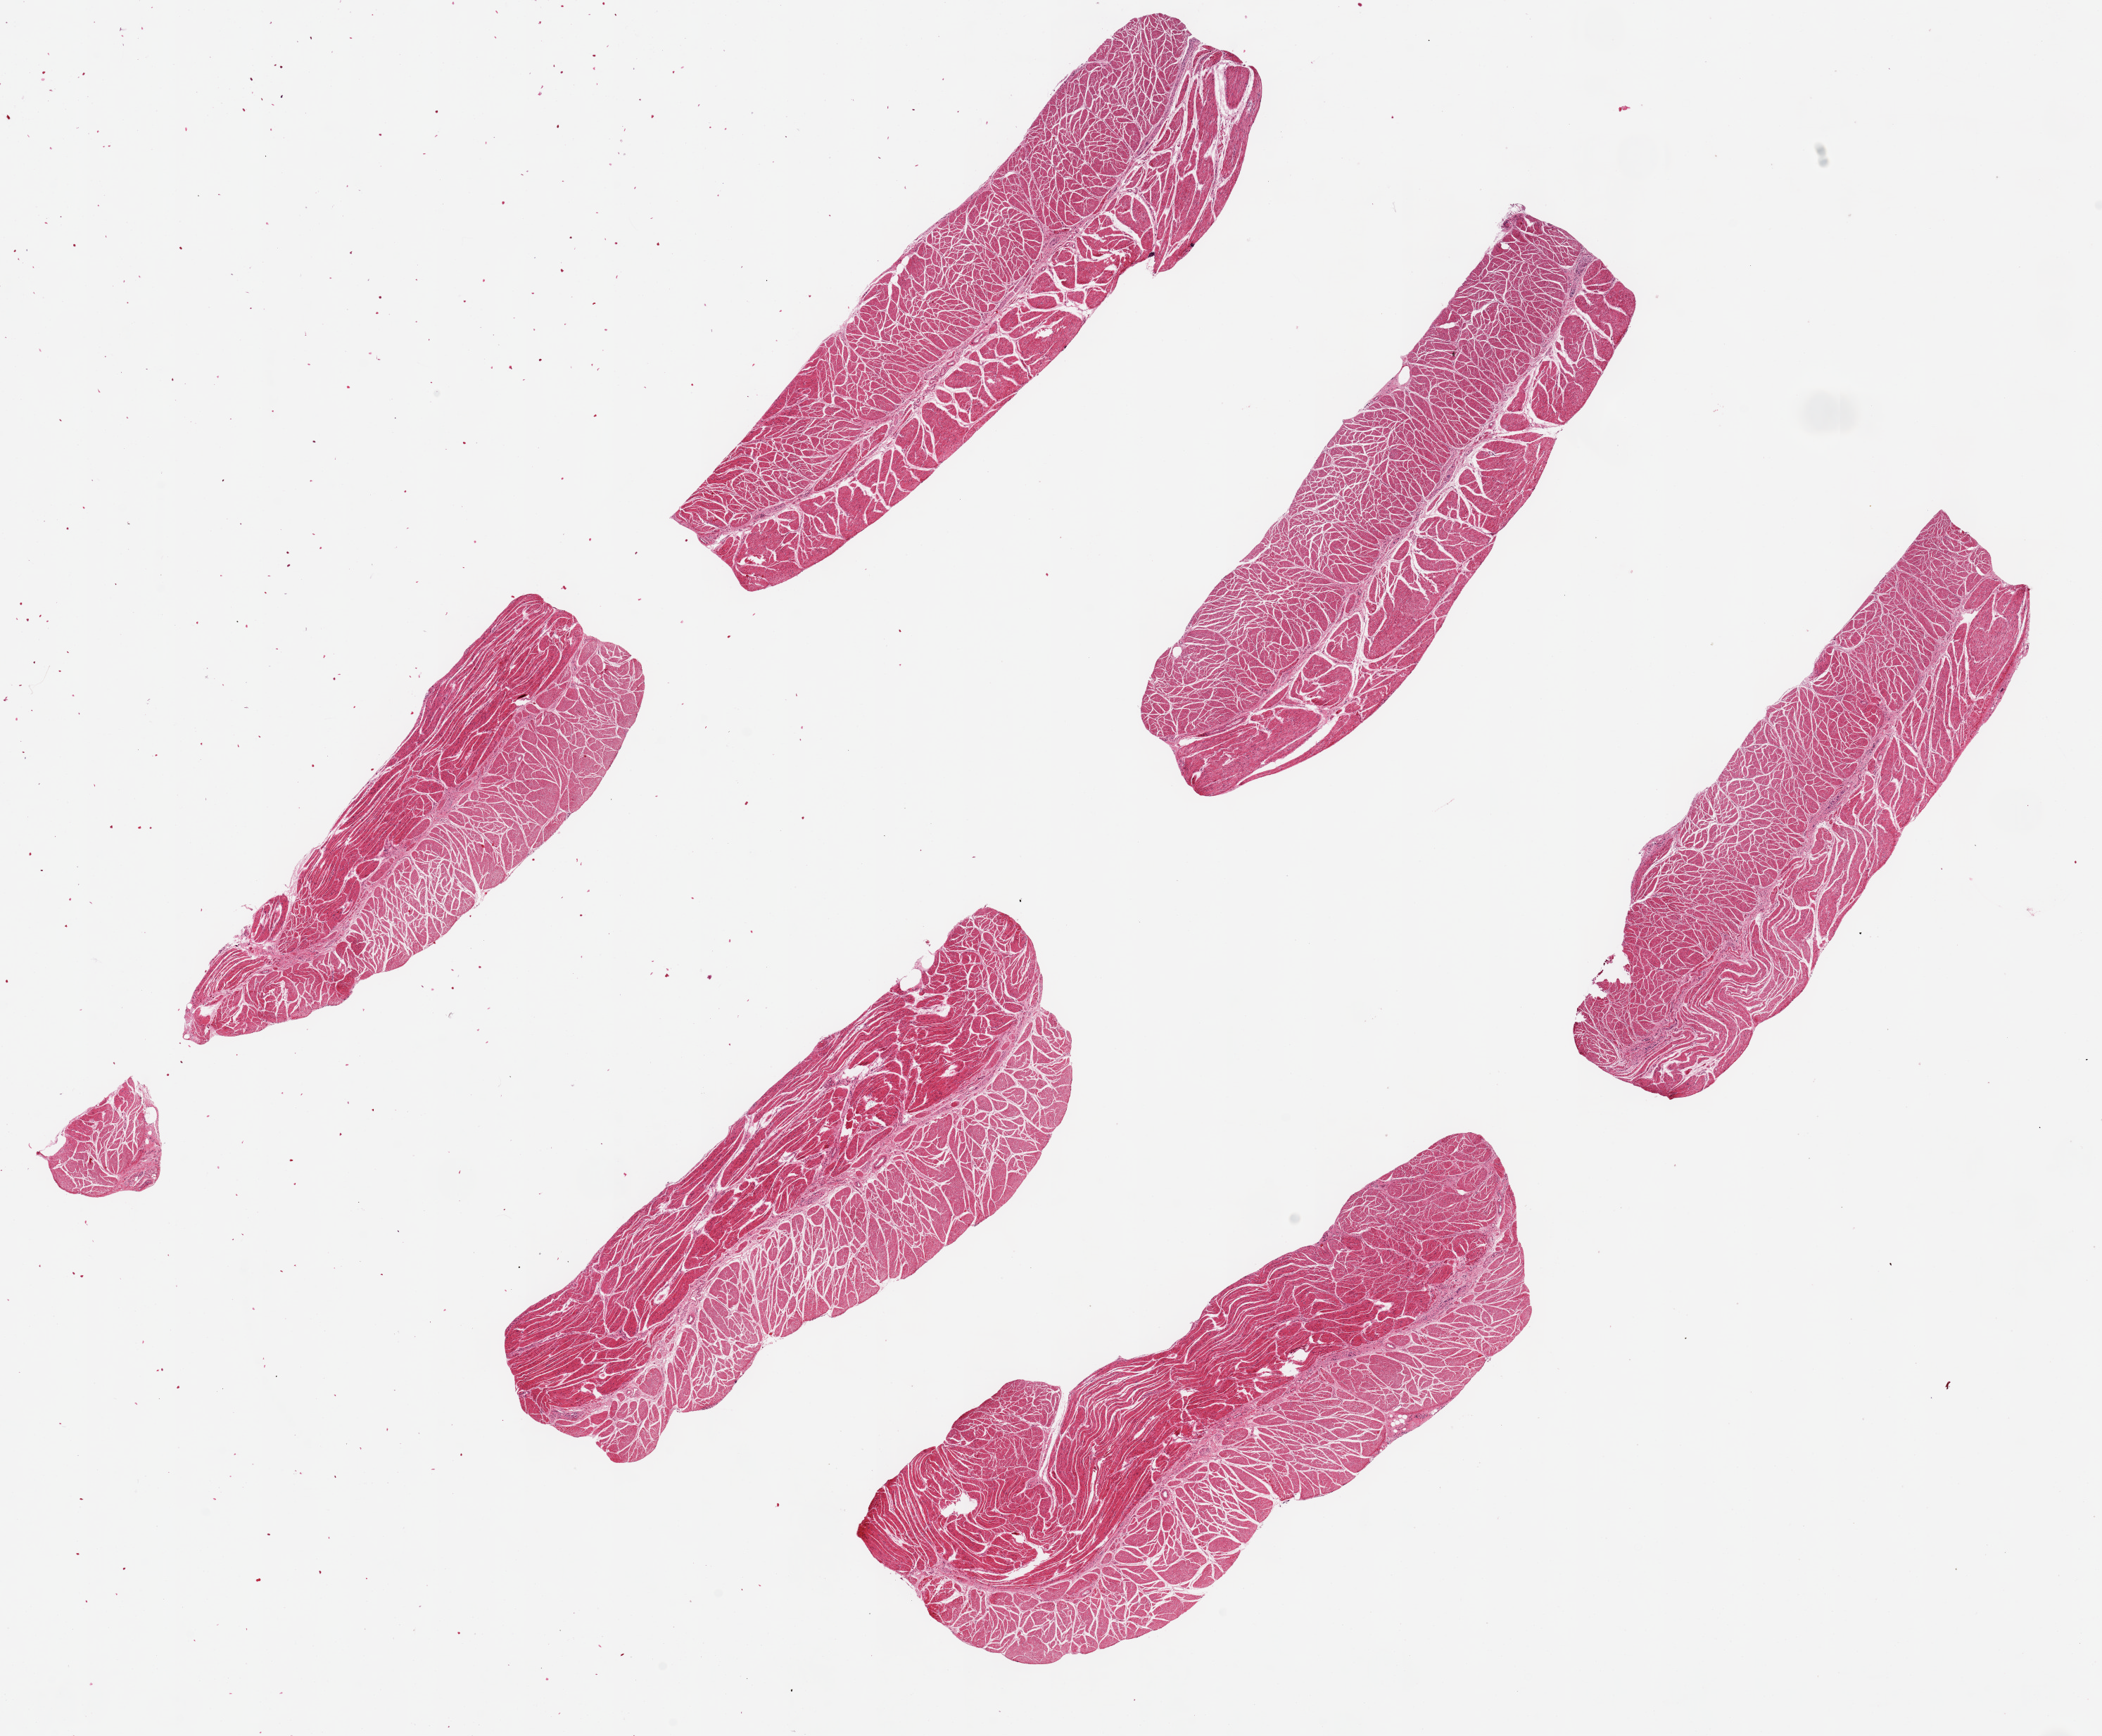
Haematoxylin and eosin whole-slide image — a low-resolution overview of the entire scanned area, about 23.6 x 19.5 mm (acquisition: 20x scan), PAXgene-fixed paraffin-embedded (PFPE) section, sampled site (target tissue): esophageal muscle, donor tissue sample. Donor: male.
* review note (as recorded): 6 ~7.5x2mm pieces